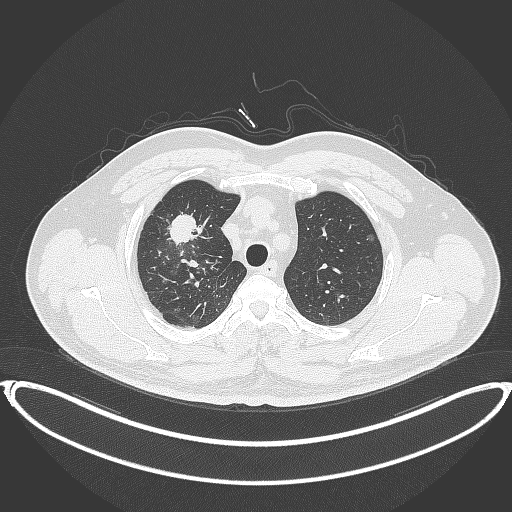
Chest CT, one axial slice. Slice 310 of 399 in the series (ordered by position). Reconstruction kernel B70f. 120 kVp. Lung window (W 1500 / L -600 HU). 512 × 512 image matrix. Male patient, age 53 years. From the clinical record (not read from this slice): clinical TNM (as recorded): T2a N0 M0.
Annotated regions visible in this slice (bounding box drawn by a radiologist):
- lung tumour (recorded histology: adenocarcinoma): box from (x=165, y=209) to (x=202, y=248) px